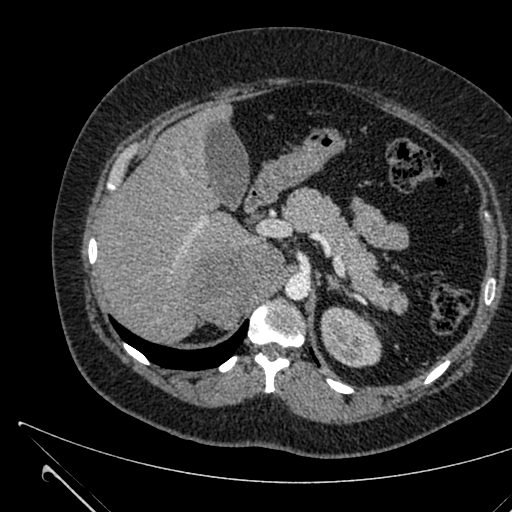
Contrast-enhanced abdominal CT, one axial slice. Position 443 of 731 along the scan axis. Soft-tissue window (W 400 / L 40 HU). 1 mm slice thickness. 512 × 512 image matrix, field of view 376 × 376 mm. Patient: female, 36 years. From the clinical record (not read from this slice): diagnosis: adrenocortical carcinoma; tumour side: right adrenal; tumour size at pathology: 10 cm; Ki-67 index: 20 %; stage (as recorded): 4.
Structures marked on this image (semi-automatic segmentation, software-assisted and operator-edited):
- mass: box from (x=193, y=243) to (x=282, y=329) px